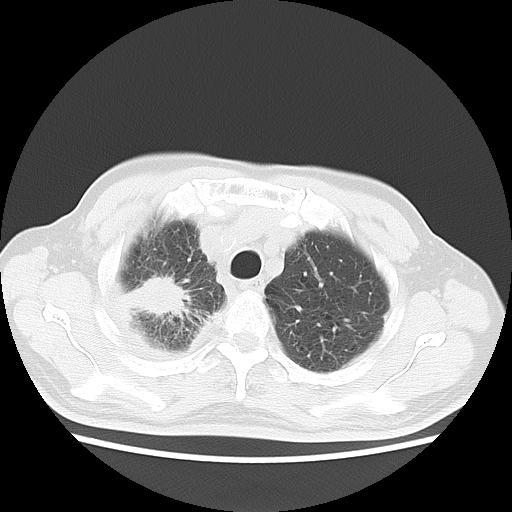
Chest CT, one axial slice; slice 15 of 16 in the series (ordered by position); lung window (W 1500 / L -600 HU); 5 mm slice thickness; 512 × 512 image matrix, field of view 350 × 350 mm. Male patient, age 75 years. From the clinical record (not read from this slice): clinical TNM (as recorded): T1c N1 M1.
Outlined on this slice (rectangle marked by the reading radiologist):
- lung tumour (recorded histology: adenocarcinoma): box from (x=125, y=271) to (x=191, y=329) px